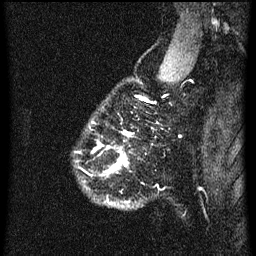
Breast MRI (dynamic contrast-enhanced), one sagittal slice. Dynamic contrast-enhanced series, image 2 of 3 at this slice position (ordered by acquisition). 1.5 T. TE 4.2 ms, TR 8.4 ms. 2 mm slice thickness. 256 × 256 image matrix. Female patient, age 34 years. From the clinical record (not read from this slice): setting: breast cancer imaged before/during neoadjuvant chemotherapy; receptor status: HR-positive, HER2-negative.
Annotated regions visible in this slice (semi-automatically segmented with operator editing):
- analysis volume of interest (the breast-tissue region the enhancement analysis was run in; not a lesion): bounding box <90,58,173,209> (left, top, right, bottom; pixels)
- tumour enhancement mask (voxels above the 70 % enhancement threshold inside the analysis volume of interest): <94,150,127,173>